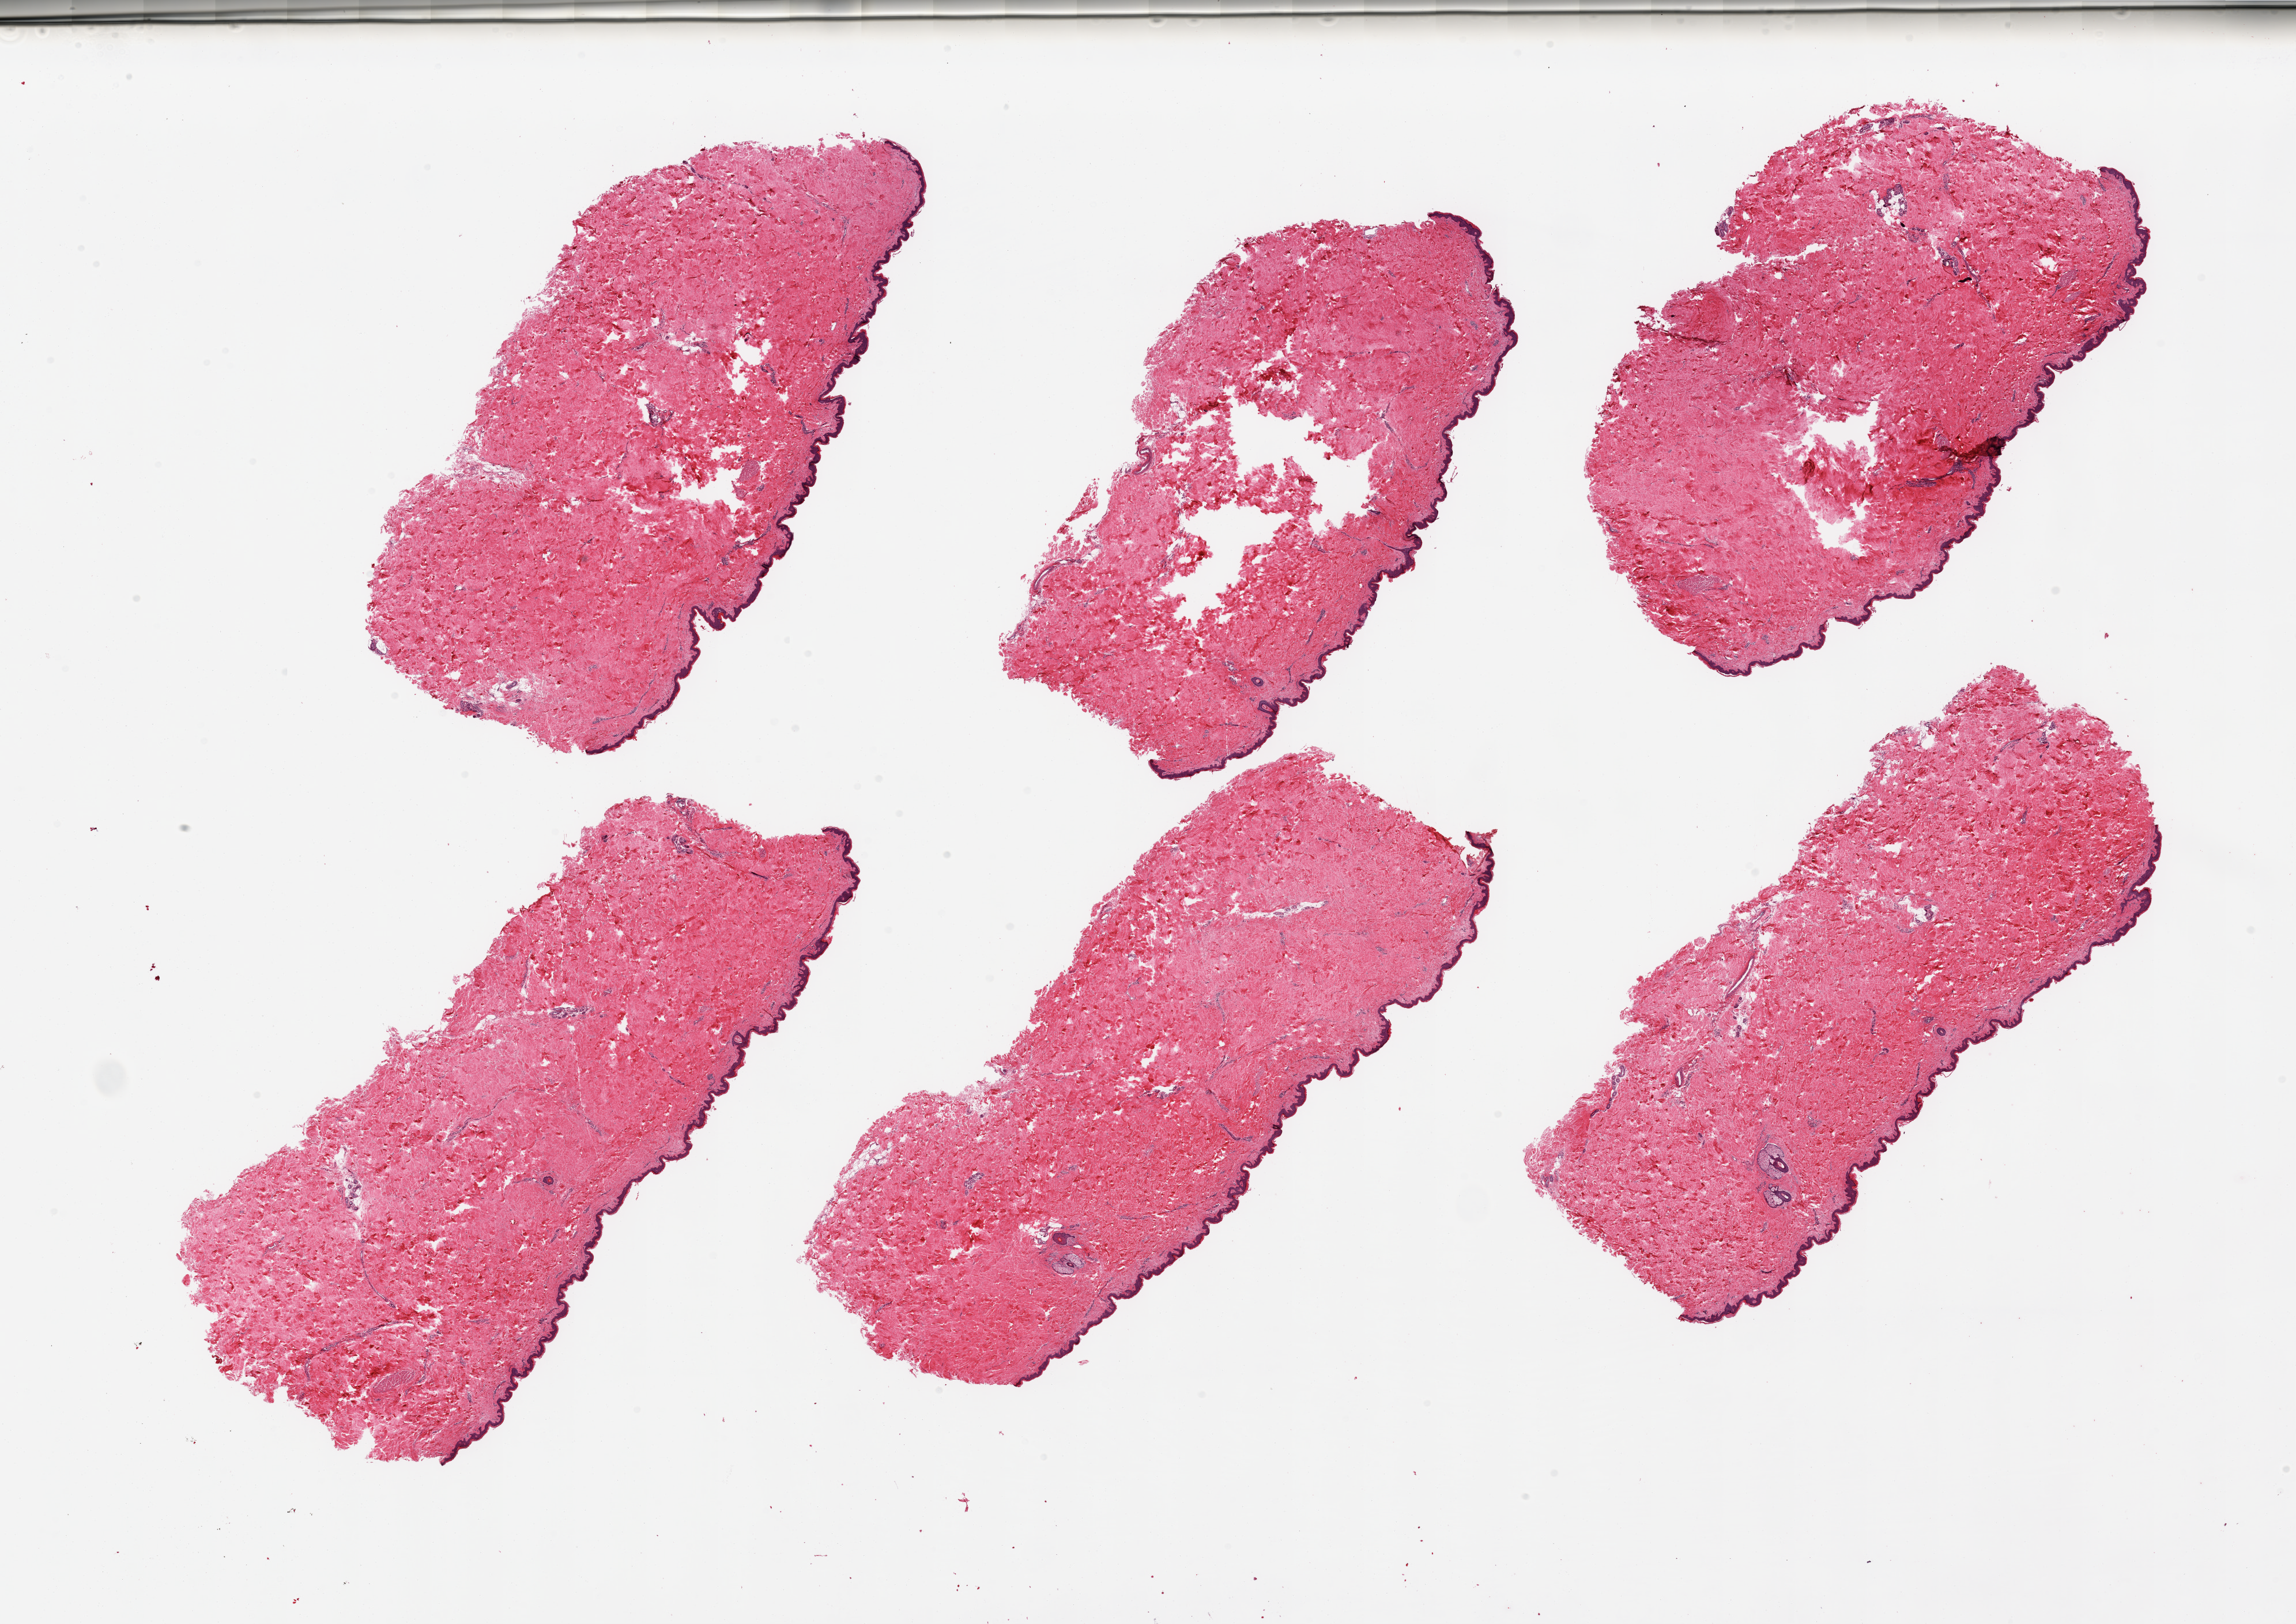
Digitized haematoxylin and eosin-stained section — whole scanned area (about 31.5 x 22.3 mm) shown as a low-resolution overview, PAXgene-fixed paraffin-embedded (PFPE) section, sampled site (target tissue): skin of suprapubic region, tissue donor sample.
Review note (as recorded): 6 pieces; well trimmed; minimal dermal fat.